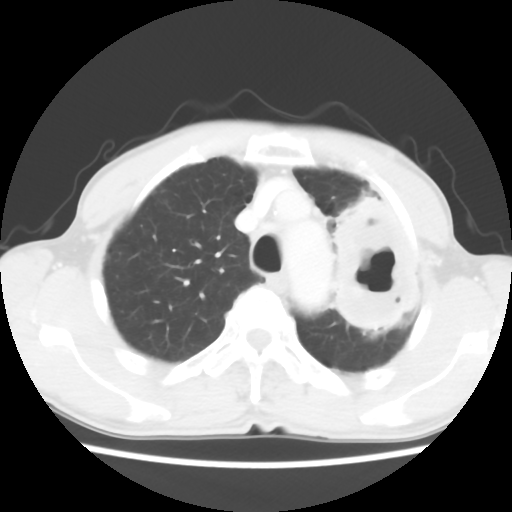
Chest CT, one axial slice. Slice 46 of 60 in the series (ordered by position). Lung window (W 1500 / L -600 HU). 512 × 512 image matrix, field of view 308 × 308 mm. Patient: male, 64 years. Case-level facts recorded for this patient, not image findings: clinical TNM (as recorded): T3 N3 M0; histopathological grade: G3.
Outlined on this slice (rectangle marked by the reading radiologist):
- lung tumour (recorded histology: adenocarcinoma): bounding box [x1, y1, x2, y2] px = [319, 189, 431, 344]